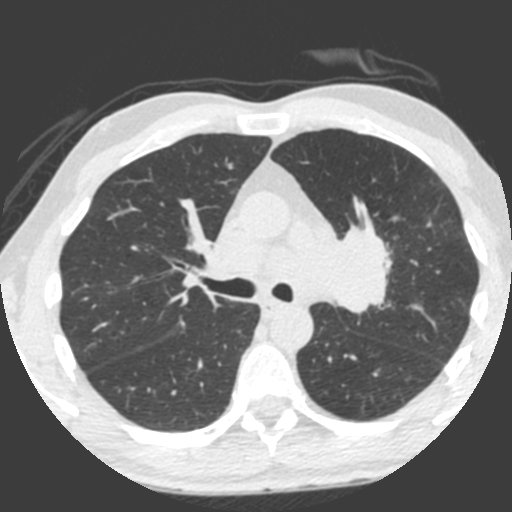
Chest CT (low-dose screening protocol), one axial image. Third screening round (two years after baseline). Lung window (W 1500 / L -600 HU). 120 kVp. Slice 140 of 212 in the series. 512 × 512 image matrix, field of view 315 × 315 mm. Male, age 55 years at enrolment. Current smoker at enrolment.
Expert reader's lesion annotation, box from (x=309, y=222) to (x=395, y=324) px. Screening reader's record for this exam (one nodule recorded; not confirmed to be the boxed lesion): non-calcified nodule or mass ≥4 mm, left upper lobe, 49 × 29 mm, spiculated (stellate) margins, soft tissue attenuation, pre-existing on the prior screen: yes; interval growth: yes. Official screen result: positive, other.